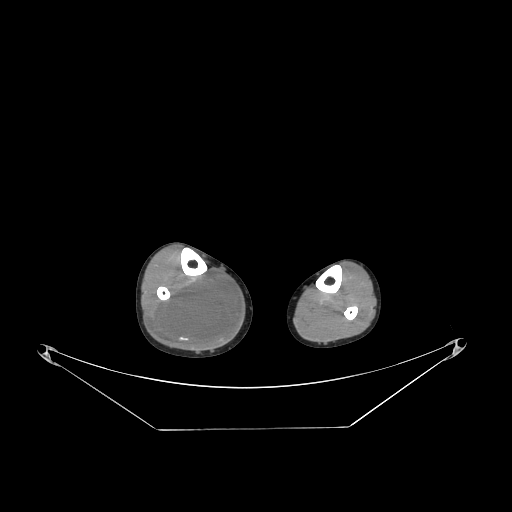
CT of an extremity soft-tissue mass (from a PET/CT study), one axial slice; slice 94 of 267 in the series (ordered by position); reconstruction kernel STANDARD; 140 kVp; soft-tissue window (W 400 / L 40 HU); 512 × 512 image matrix. Male patient. Case-level facts recorded for this patient, not image findings: histological type: liposarcoma - round cell; grade: high; site of the primary tumour: right calf.
Outlined on this slice (expert contour drawn on MRI and transferred to this co-registered scan by the dataset authors):
- gross tumour volume (mass): bounding box <153,272,241,350> (left, top, right, bottom; pixels)